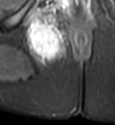
MRI of an extremity soft-tissue mass, one axial slice; slice 30 of 49 in the series (ordered by position); STIR; MR volume resampled by the dataset authors to the PET/CT grid (not the native acquisition matrix); 115 × 125 image matrix, field of view 112 × 122 mm. Female patient. Case-level facts recorded for this patient, not image findings: histological type: epithelioid sarcoma; grade: intermediate; site of the primary tumour: right buttock.
Outlined on this slice (expert contour drawn on MRI and transferred to this co-registered scan by the dataset authors):
- gross tumour volume including surrounding oedema: bounding box [x1, y1, x2, y2] px = [26, 14, 66, 63]
- gross tumour volume (mass): [29, 21, 59, 58]